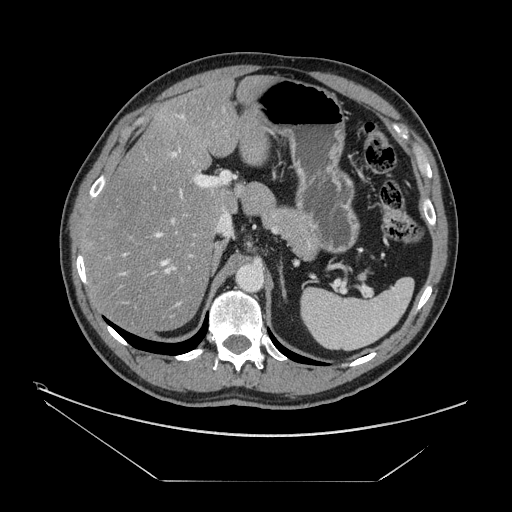
Contrast-enhanced abdominal CT, one axial slice. Position 95 of 161 along the scan axis. Reconstruction kernel STANDARD. 120 kVp. Intravenous contrast given. Soft-tissue window (W 400 / L 40 HU). 2.5 mm slice thickness. 512 × 512 image matrix. Male patient, age 65 years. From the clinical record (not read from this slice): diagnosis: colorectal cancer liver metastases, imaged before liver resection; multiple liver metastases: yes; largest metastasis: 4.2 cm.
Annotated regions visible in this slice (manually delineated by an expert):
- hepatic veins: box from (x=120, y=116) to (x=183, y=276) px
- liver: (x=85, y=78)–(x=273, y=330)
- planned liver remnant (the part of the liver to remain after resection): (x=85, y=78)–(x=273, y=330)
- portal vein (with intrahepatic branches): (x=119, y=149)–(x=229, y=318)